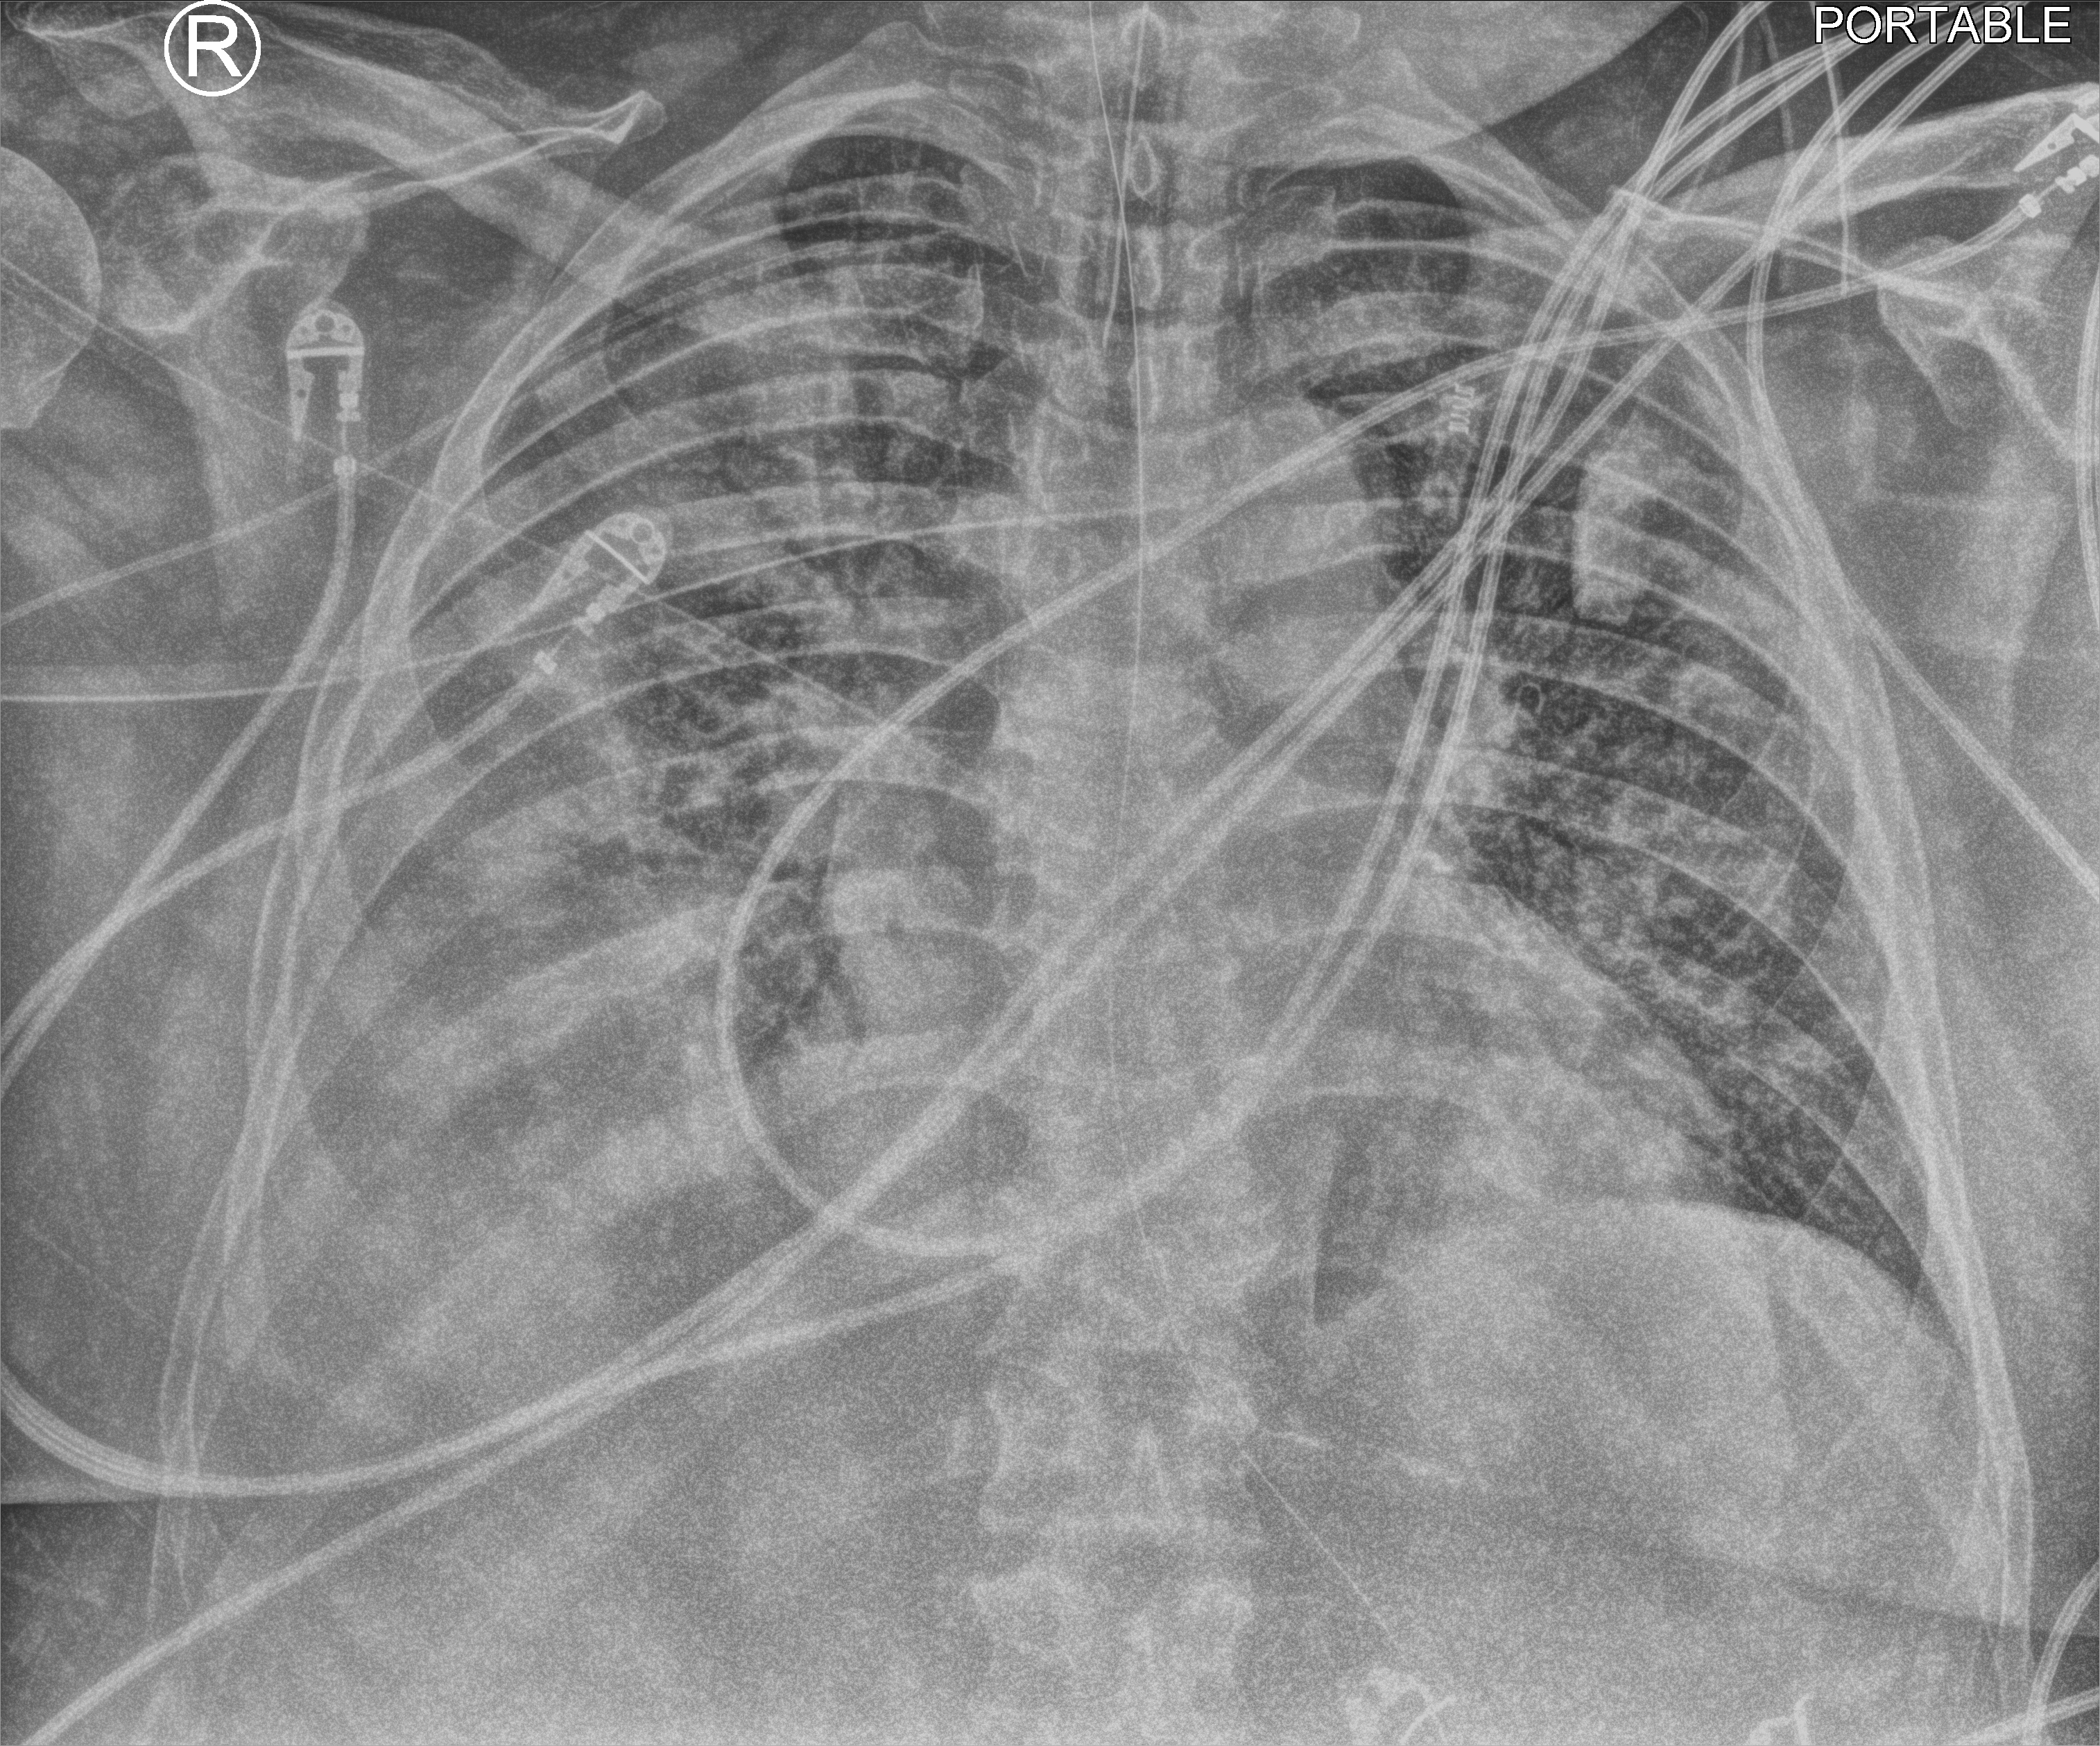
Chest X-ray (portable), anteroposterior (AP) projection. Male patient hospitalised with COVID-19, age 18–59 years.
Admission-level facts for this patient (not findings on this image; timing relative to this image not recorded): mechanically ventilated during this hospital stay: yes.